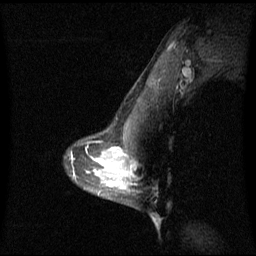
Breast MRI (dynamic contrast-enhanced), one sagittal slice; slice 46 of 60 in the series (ordered by position); dynamic contrast-enhanced series, image 2 of 3 at this slice position (ordered by acquisition); 1.5 T; TE 4.2 ms, TR 8.4 ms; 256 × 256 image matrix. Patient: female, 42 years. From the clinical record (not read from this slice): setting: breast cancer imaged before/during neoadjuvant chemotherapy; receptor status: triple-negative.
Annotated regions visible in this slice (semi-automatically segmented with operator editing):
- analysis volume of interest (the breast-tissue region the enhancement analysis was run in; not a lesion): bounding box <106,156,131,187> (left, top, right, bottom; pixels)
- tumour enhancement mask (voxels above the 70 % enhancement threshold inside the analysis volume of interest): <121,172,130,187>